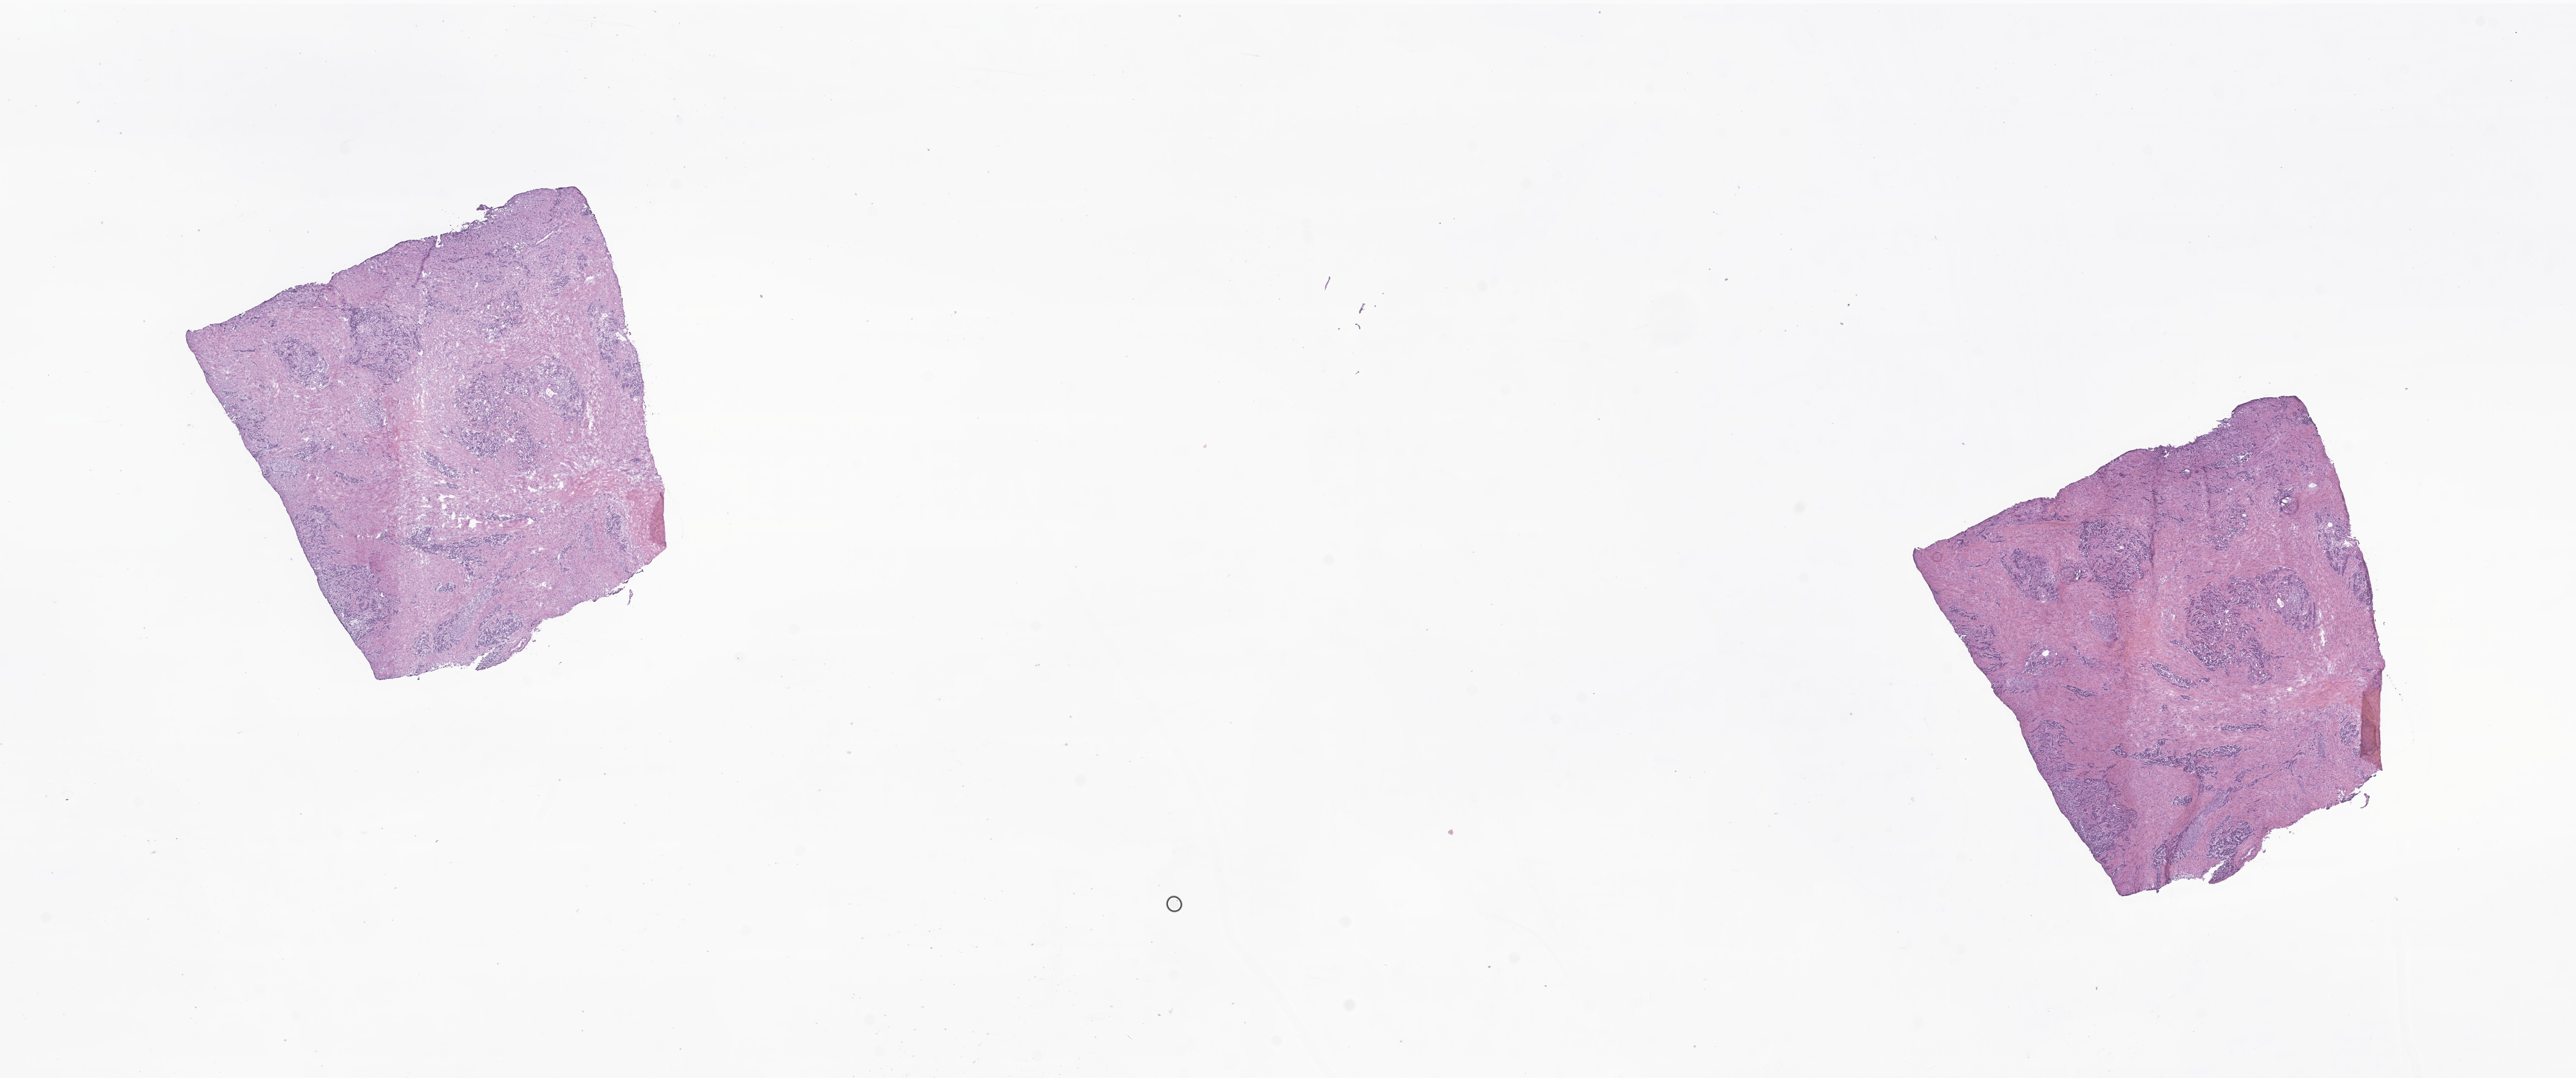
Hematoxylin and eosin (H&E) whole-slide image of tumor tissue from the head of pancreas, low-resolution overview of the scanned area, about 25.7 x 10.8 mm; frozen section (OCT-embedded). Male patient, age 211 months (17 years 7 months).
• diagnosis: Neuroendocrine tumor, NOS